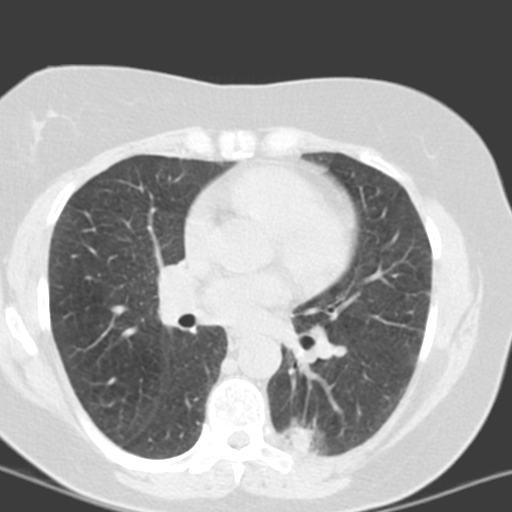
Low-dose screening chest CT, one axial slice. Lung window (W 1500 / L -600 HU). 512 × 512 image matrix, field of view 290 × 290 mm.
Structures marked on this image (outlined manually by an expert reader):
- lesion 2 (tumor, lower lobe of left lung): bounding box [x1, y1, x2, y2] px = [292, 427, 318, 449]